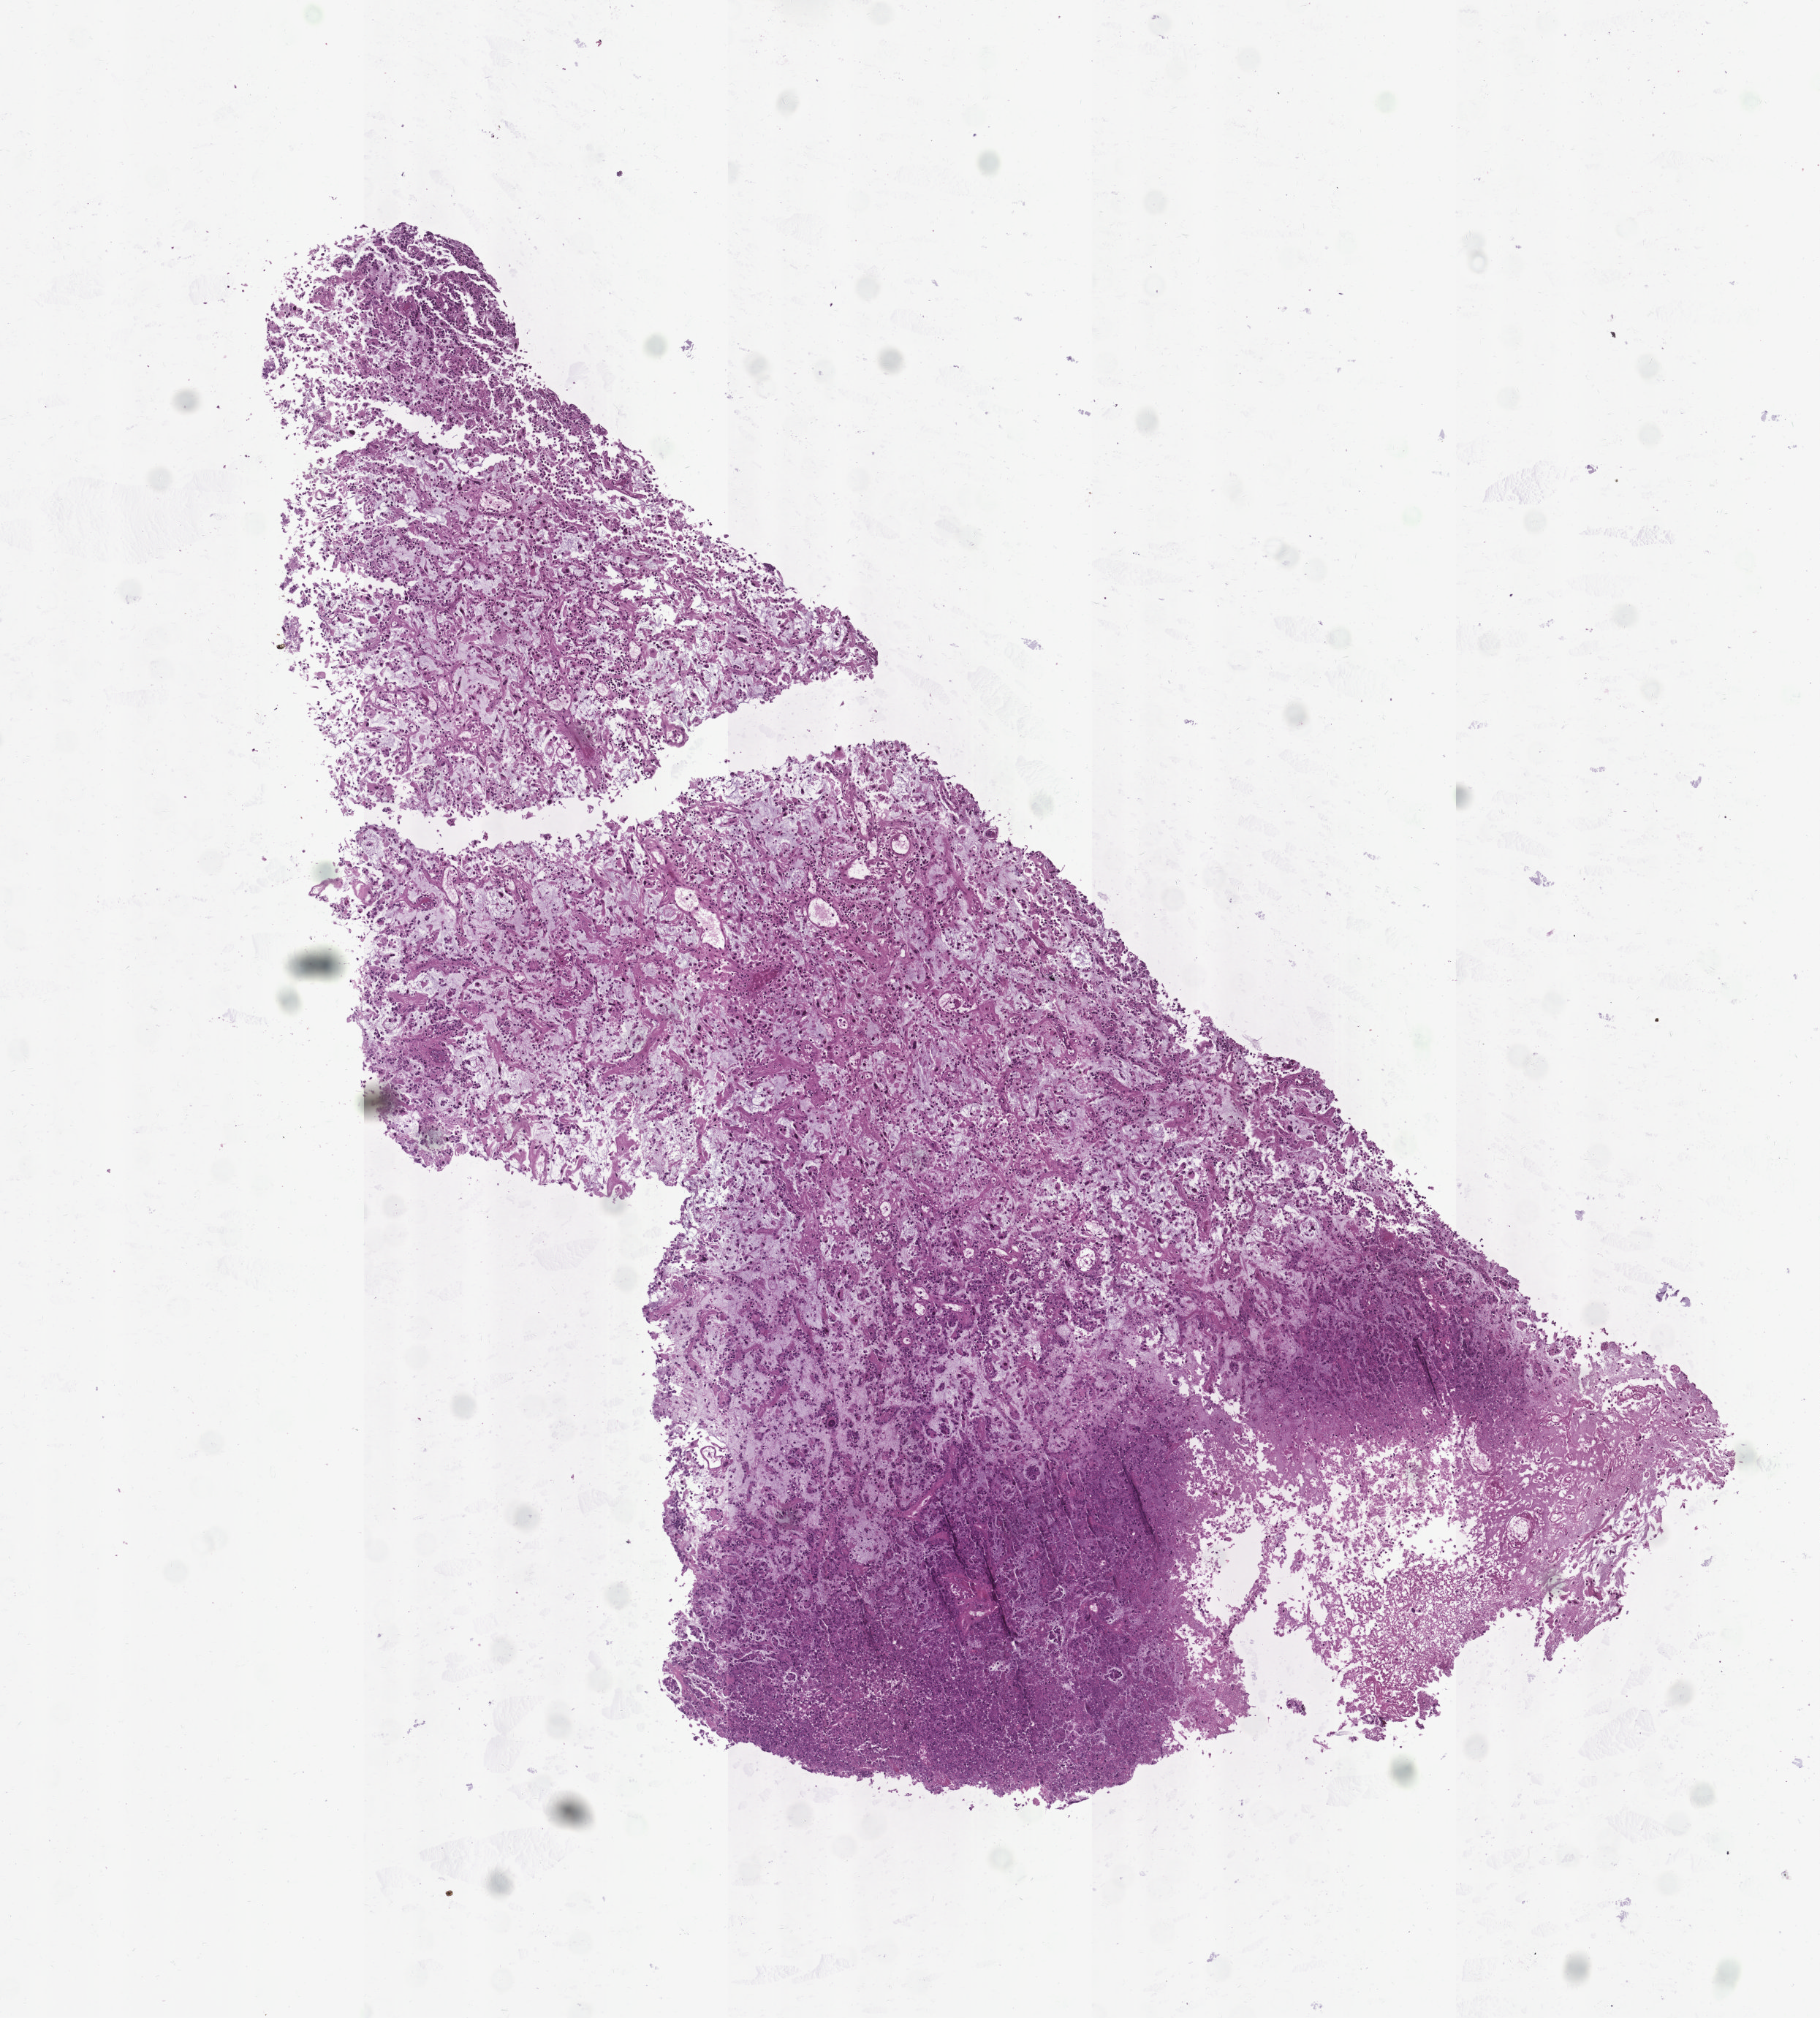
Digitized Hematoxylin and eosin (H&E) stained tissue section (whole slide), shown as a low-resolution overview of the whole scanned area (about 5.0 x 5.6 mm, slide scanned at 20x). Tumour tissue sample, brain. 35-year-old male patient.
Histologic diagnosis: Glioblastoma.